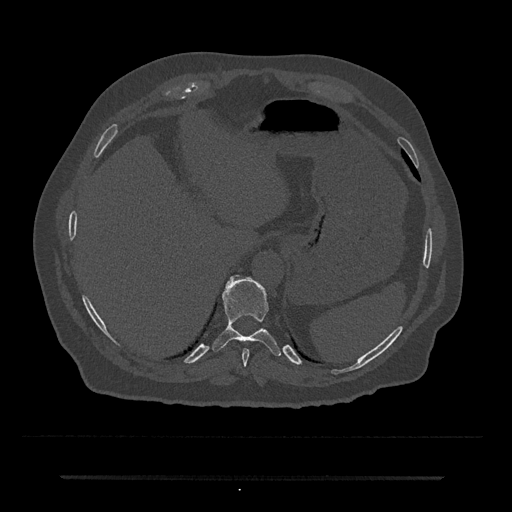
CT including the spine, one axial slice; position 235 of 797 along the scan axis; reconstruction kernel Br40s/3; bone window (W 1800 / L 400 HU); 0.5 mm slice thickness; 512 × 512 image matrix. Male patient, age 69 years. Case-level facts recorded for this patient, not image findings: primary cancer: prostate.
Annotated regions visible in this slice (semi-automatically segmented with operator editing):
- T10 vertebra: bounding box [x1, y1, x2, y2] px = [212, 275, 281, 356]
- T9 vertebra: [242, 348, 250, 366]